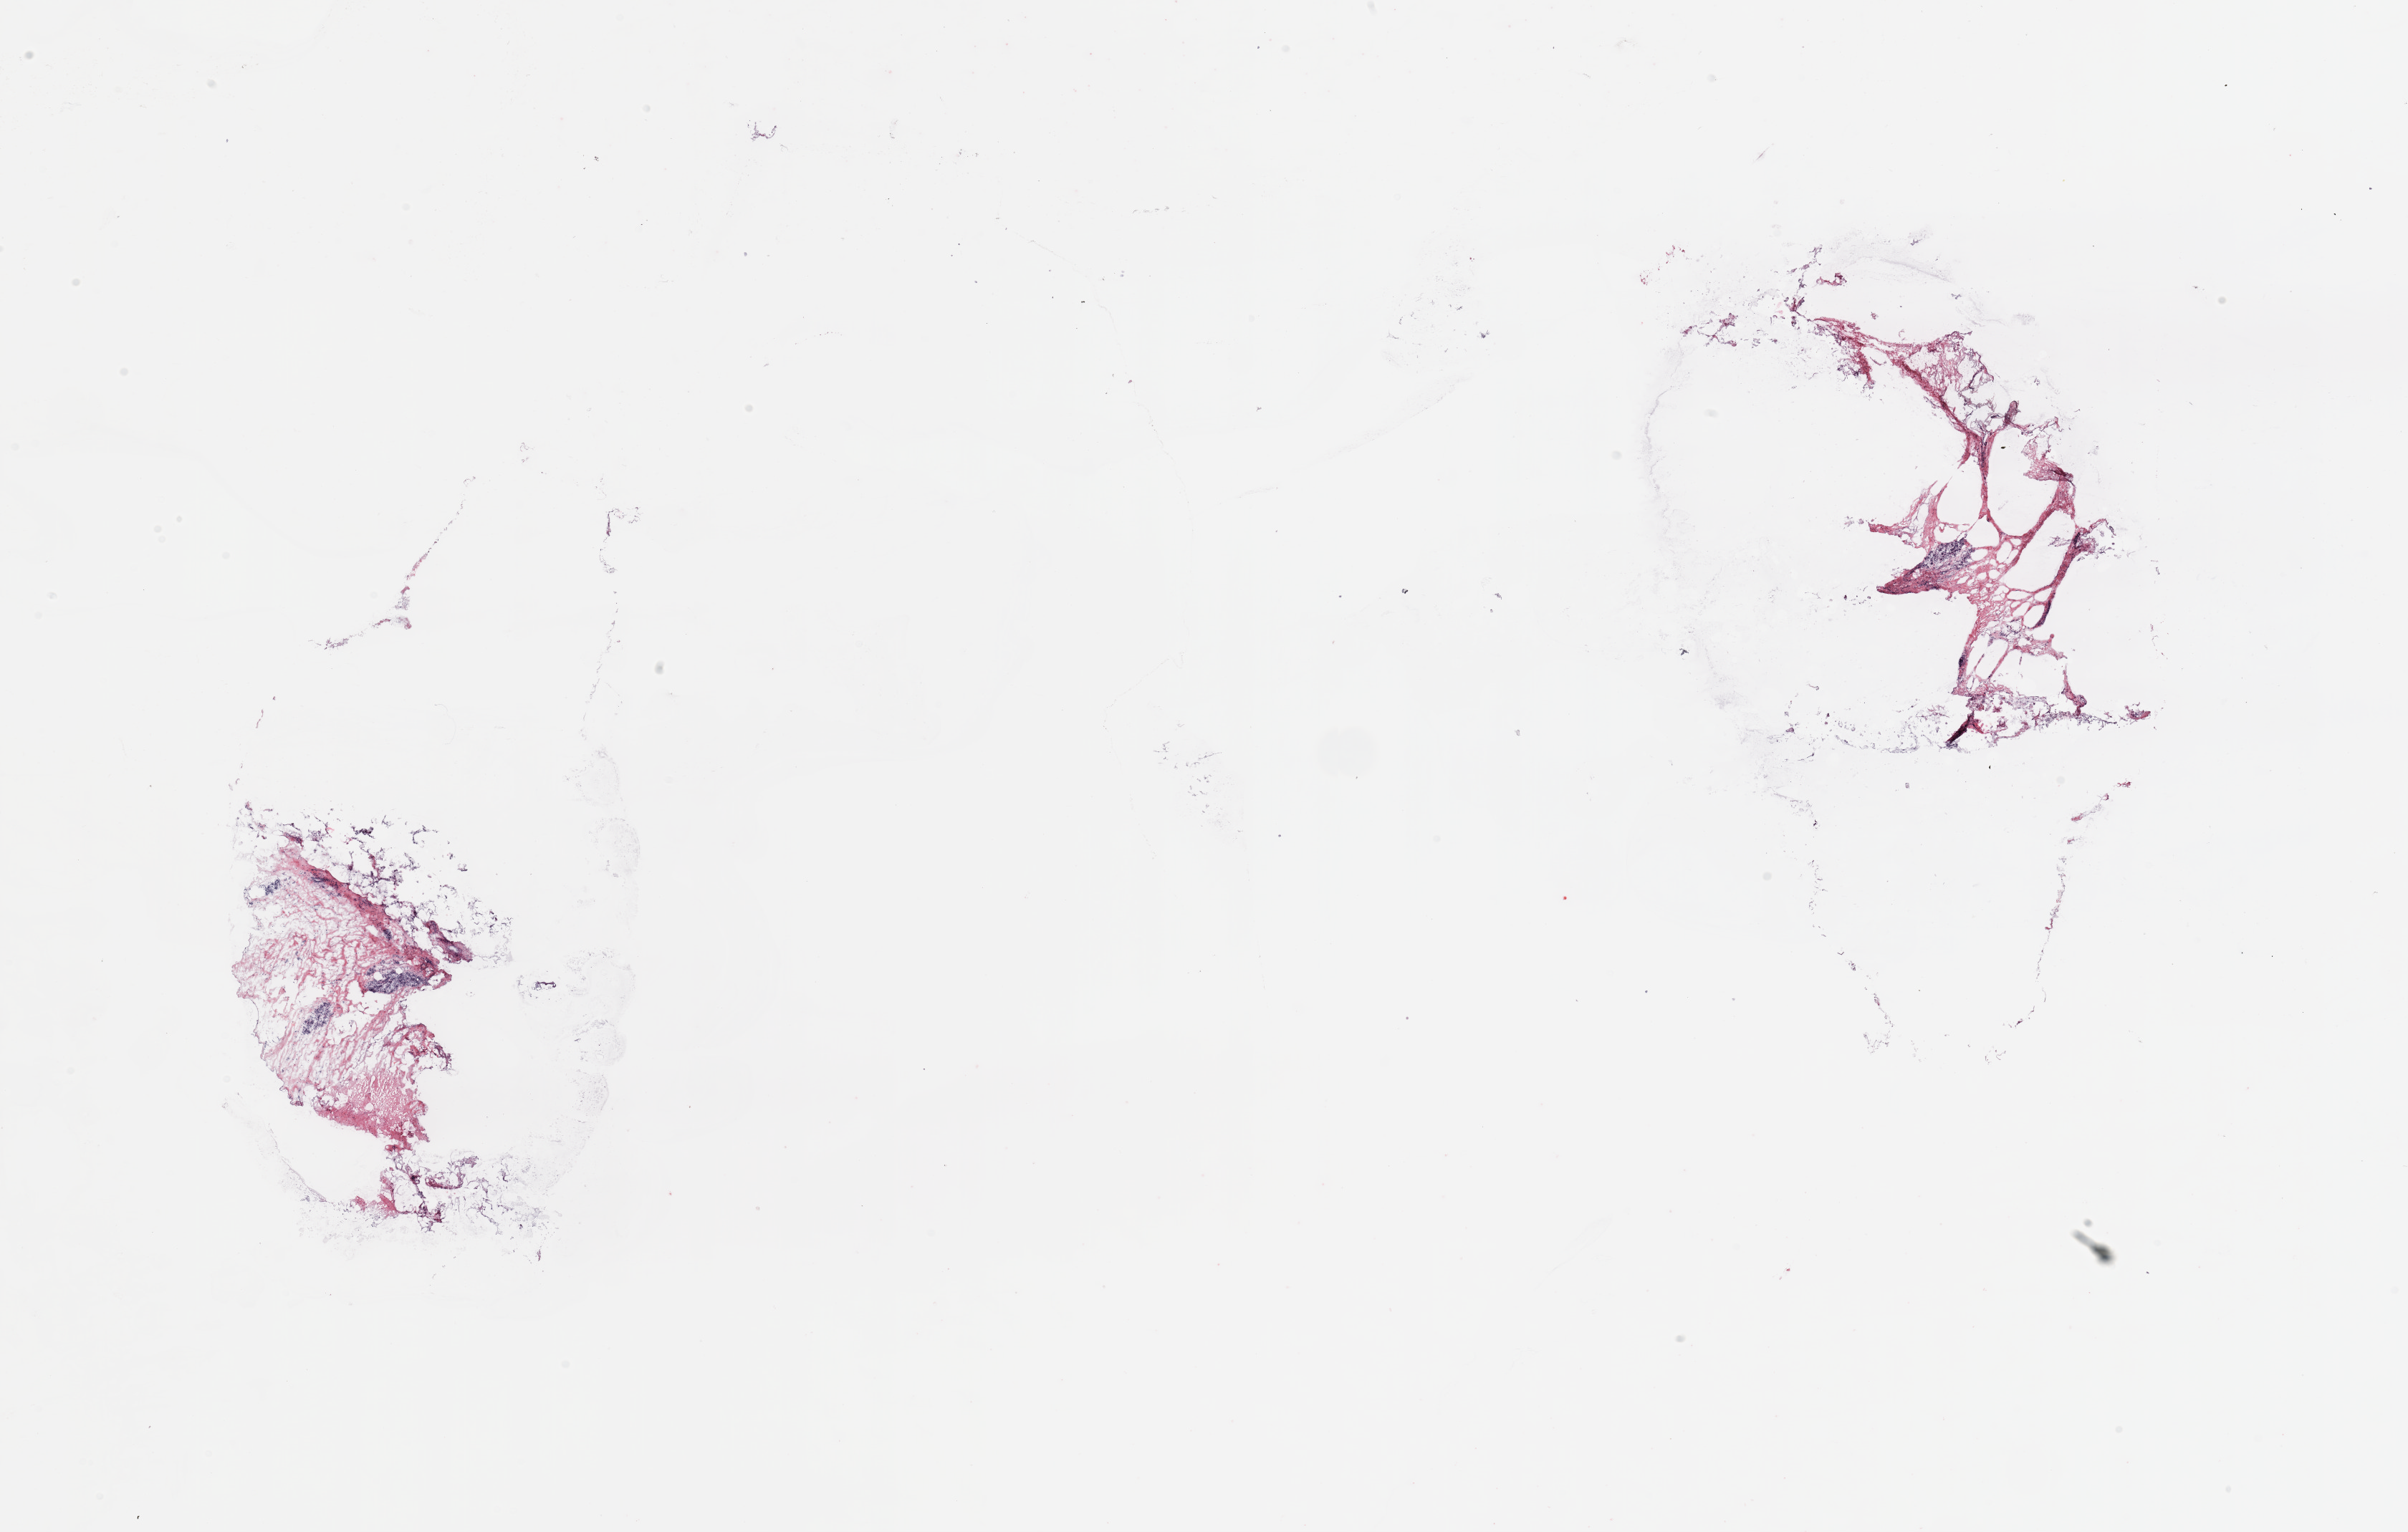
H&E-stained whole-slide image — shown as a low-resolution overview of the whole scanned area (about 26.6 x 16.9 mm). Breast, tumour tissue. Female, 35 y/o.
Histologic diagnosis: Infiltrating duct carcinoma, NOS.